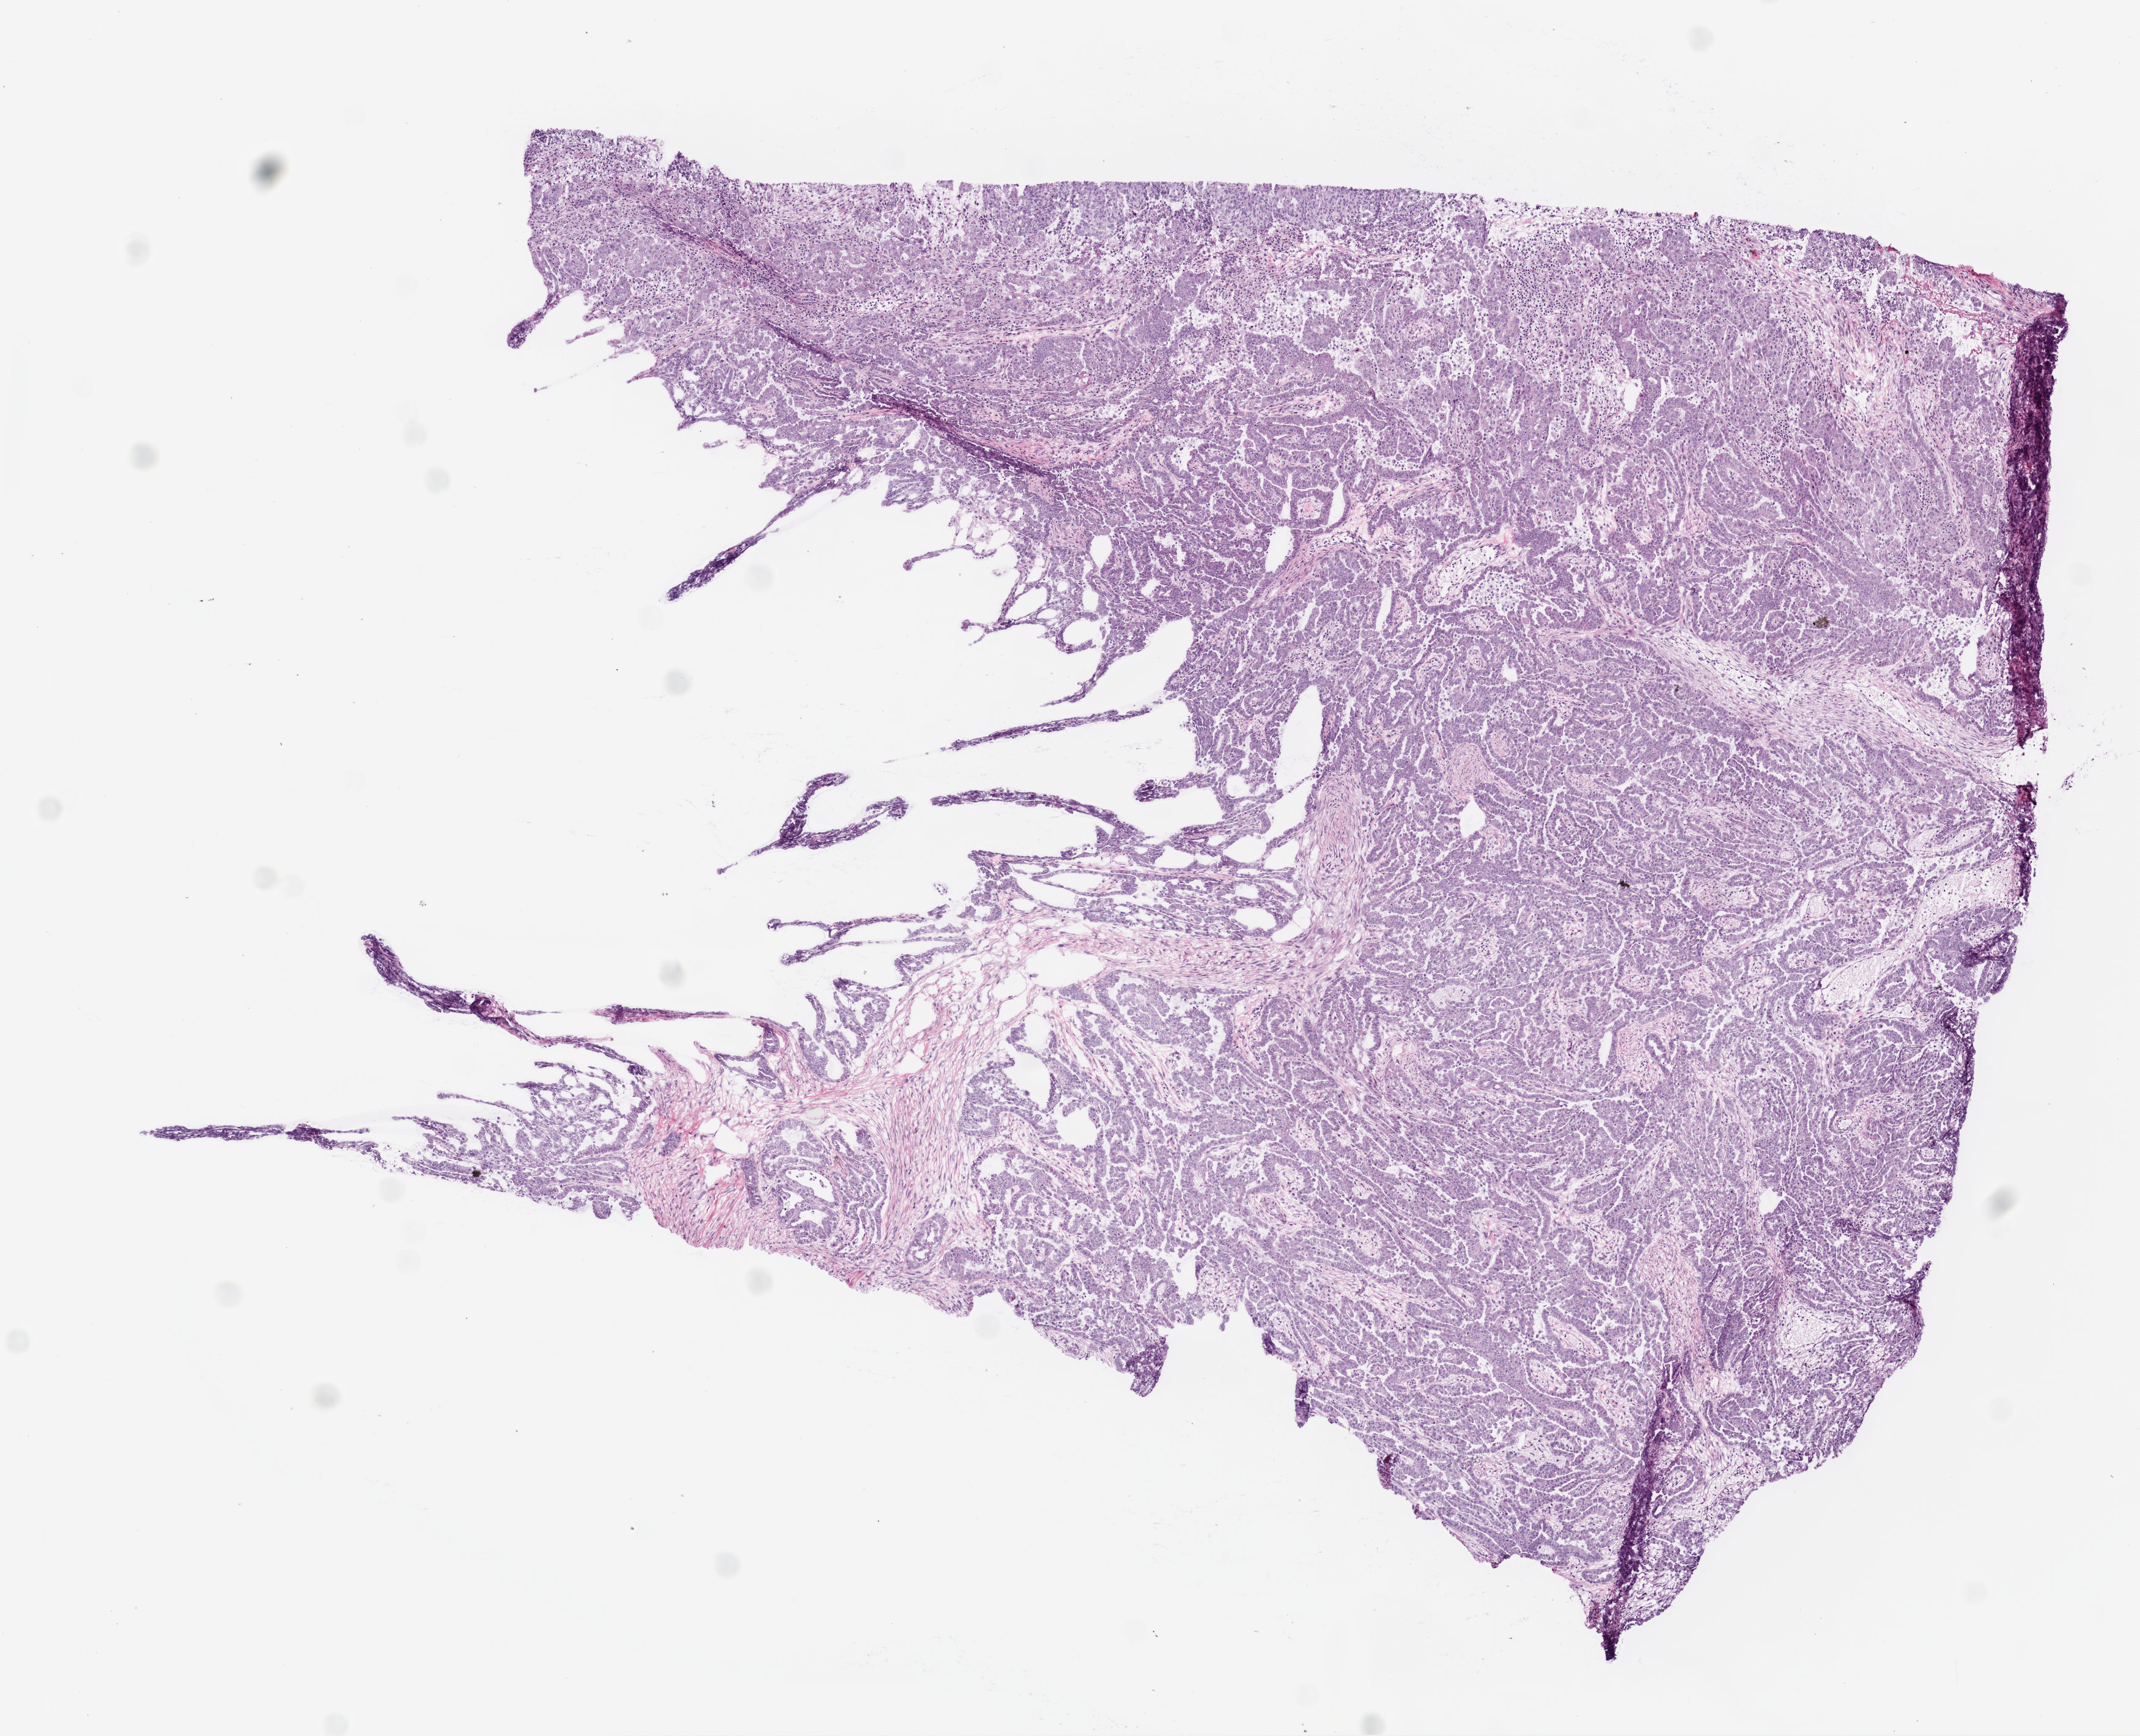
Digitized H&E-stained tissue section (whole slide), low-resolution overview of the scanned area, about 7.0 x 5.7 mm (from a 20x scan). Frozen section from the bottom of the tissue portion. Primary tumour sample from the ovary. Patient: female, age at initial diagnosis 59 years. Histologic grade: G3 (poorly differentiated). Slide review estimates, as recorded: tumour cells 87%, tumour nuclei 85%, normal cells 0%, stromal cells 10%, necrosis 3%.
• histologic diagnosis: Serous cystadenocarcinoma, NOS
• laterality: bilateral
• FIGO stage: IIIB